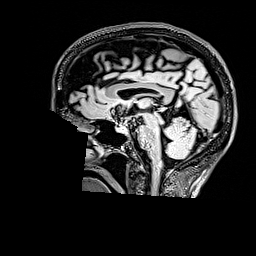
Brain MRI from a brain-tumour surgery series, one sagittal slice. T2 FLAIR. 256 × 256 image matrix, field of view 256 × 256 mm. From the clinical record (not read from this slice): histopathology: Astrocytoma; WHO grade: 3; IDH mutation: yes; tumour location: Right Parietal.
Annotated regions visible in this slice (outlined manually by an expert reader):
- tumour: bounding box <187,59,202,71> (left, top, right, bottom; pixels)
- tumour: <188,59,202,71>